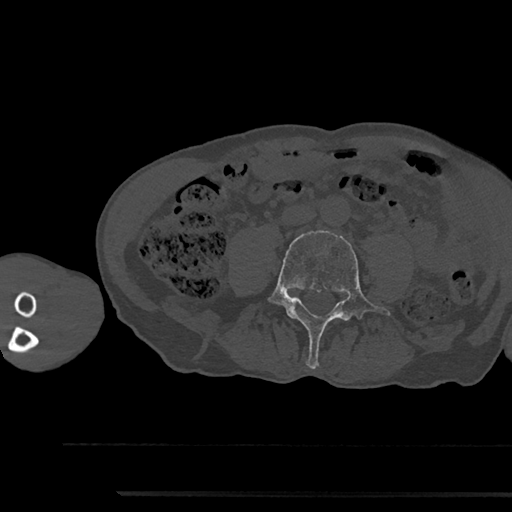
CT including the spine, one axial slice; position 414 of 797 along the scan axis; reconstruction kernel Br40s/3; 120 kVp; bone window (W 1800 / L 400 HU); 512 × 512 image matrix. Male patient, age 79 years. From the clinical record (not read from this slice): primary cancer: prostate.
Structures marked on this image (semi-automatic segmentation, software-assisted and operator-edited):
- L4 vertebra: bounding box (x1, y1, x2, y2) in pixels: (268, 230, 391, 369)